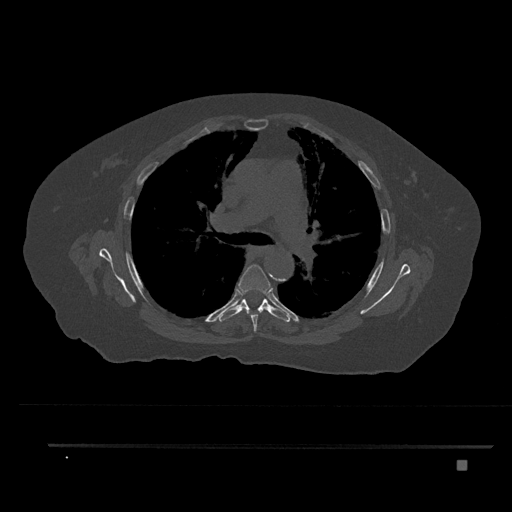
CT including the spine, one axial slice; slice 547 of 797 in the series (ordered by position); 120 kVp; bone window (W 1800 / L 400 HU); 0.5 mm slice thickness; 512 × 512 image matrix. Female patient, age 76 years. From the clinical record (not read from this slice): primary cancer: lung.
Outlined on this slice (semi-automatic segmentation, software-assisted and operator-edited):
- T5 vertebra: box from (x=238, y=264) to (x=271, y=332) px
- T6 vertebra: (x=219, y=289)–(x=290, y=322)